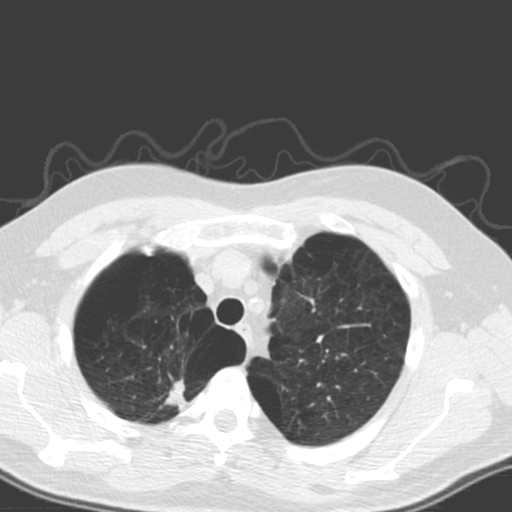
Low-dose screening chest CT, one axial slice; position 141 of 173 along the scan axis; 120 kVp; lung window (W 1500 / L -600 HU); 3.2 mm slice thickness; 512 × 512 image matrix, field of view 340 × 340 mm.
Annotated regions visible in this slice (outlined manually by an expert reader):
- lesion 1 (tumor, upper lobe of right lung): bounding box (x1, y1, x2, y2) in pixels: (164, 379, 188, 410)